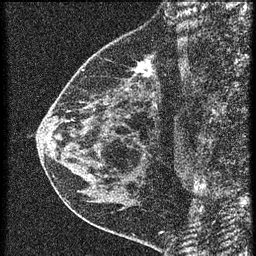
Breast MRI (dynamic contrast-enhanced), one sagittal slice; slice 22 of 60 in the series (ordered by position); 3 images stored at this slice position (order not interpretable as contrast timing); 1.5 T; TE 4.2 ms, TR 20.4 ms; 256 × 256 image matrix, field of view 180 × 180 mm. Patient: female, 46 years. Case-level facts recorded for this patient, not image findings: setting: breast cancer imaged before/during neoadjuvant chemotherapy; receptor status: HR-positive, HER2-negative.
Outlined on this slice (semi-automatic segmentation, software-assisted and operator-edited):
- analysis volume of interest (the breast-tissue region the enhancement analysis was run in; not a lesion): box from (x=58, y=36) to (x=169, y=155) px
- tumour enhancement mask (voxels above the 90 % enhancement threshold inside the analysis volume of interest): (x=138, y=62)–(x=151, y=75)